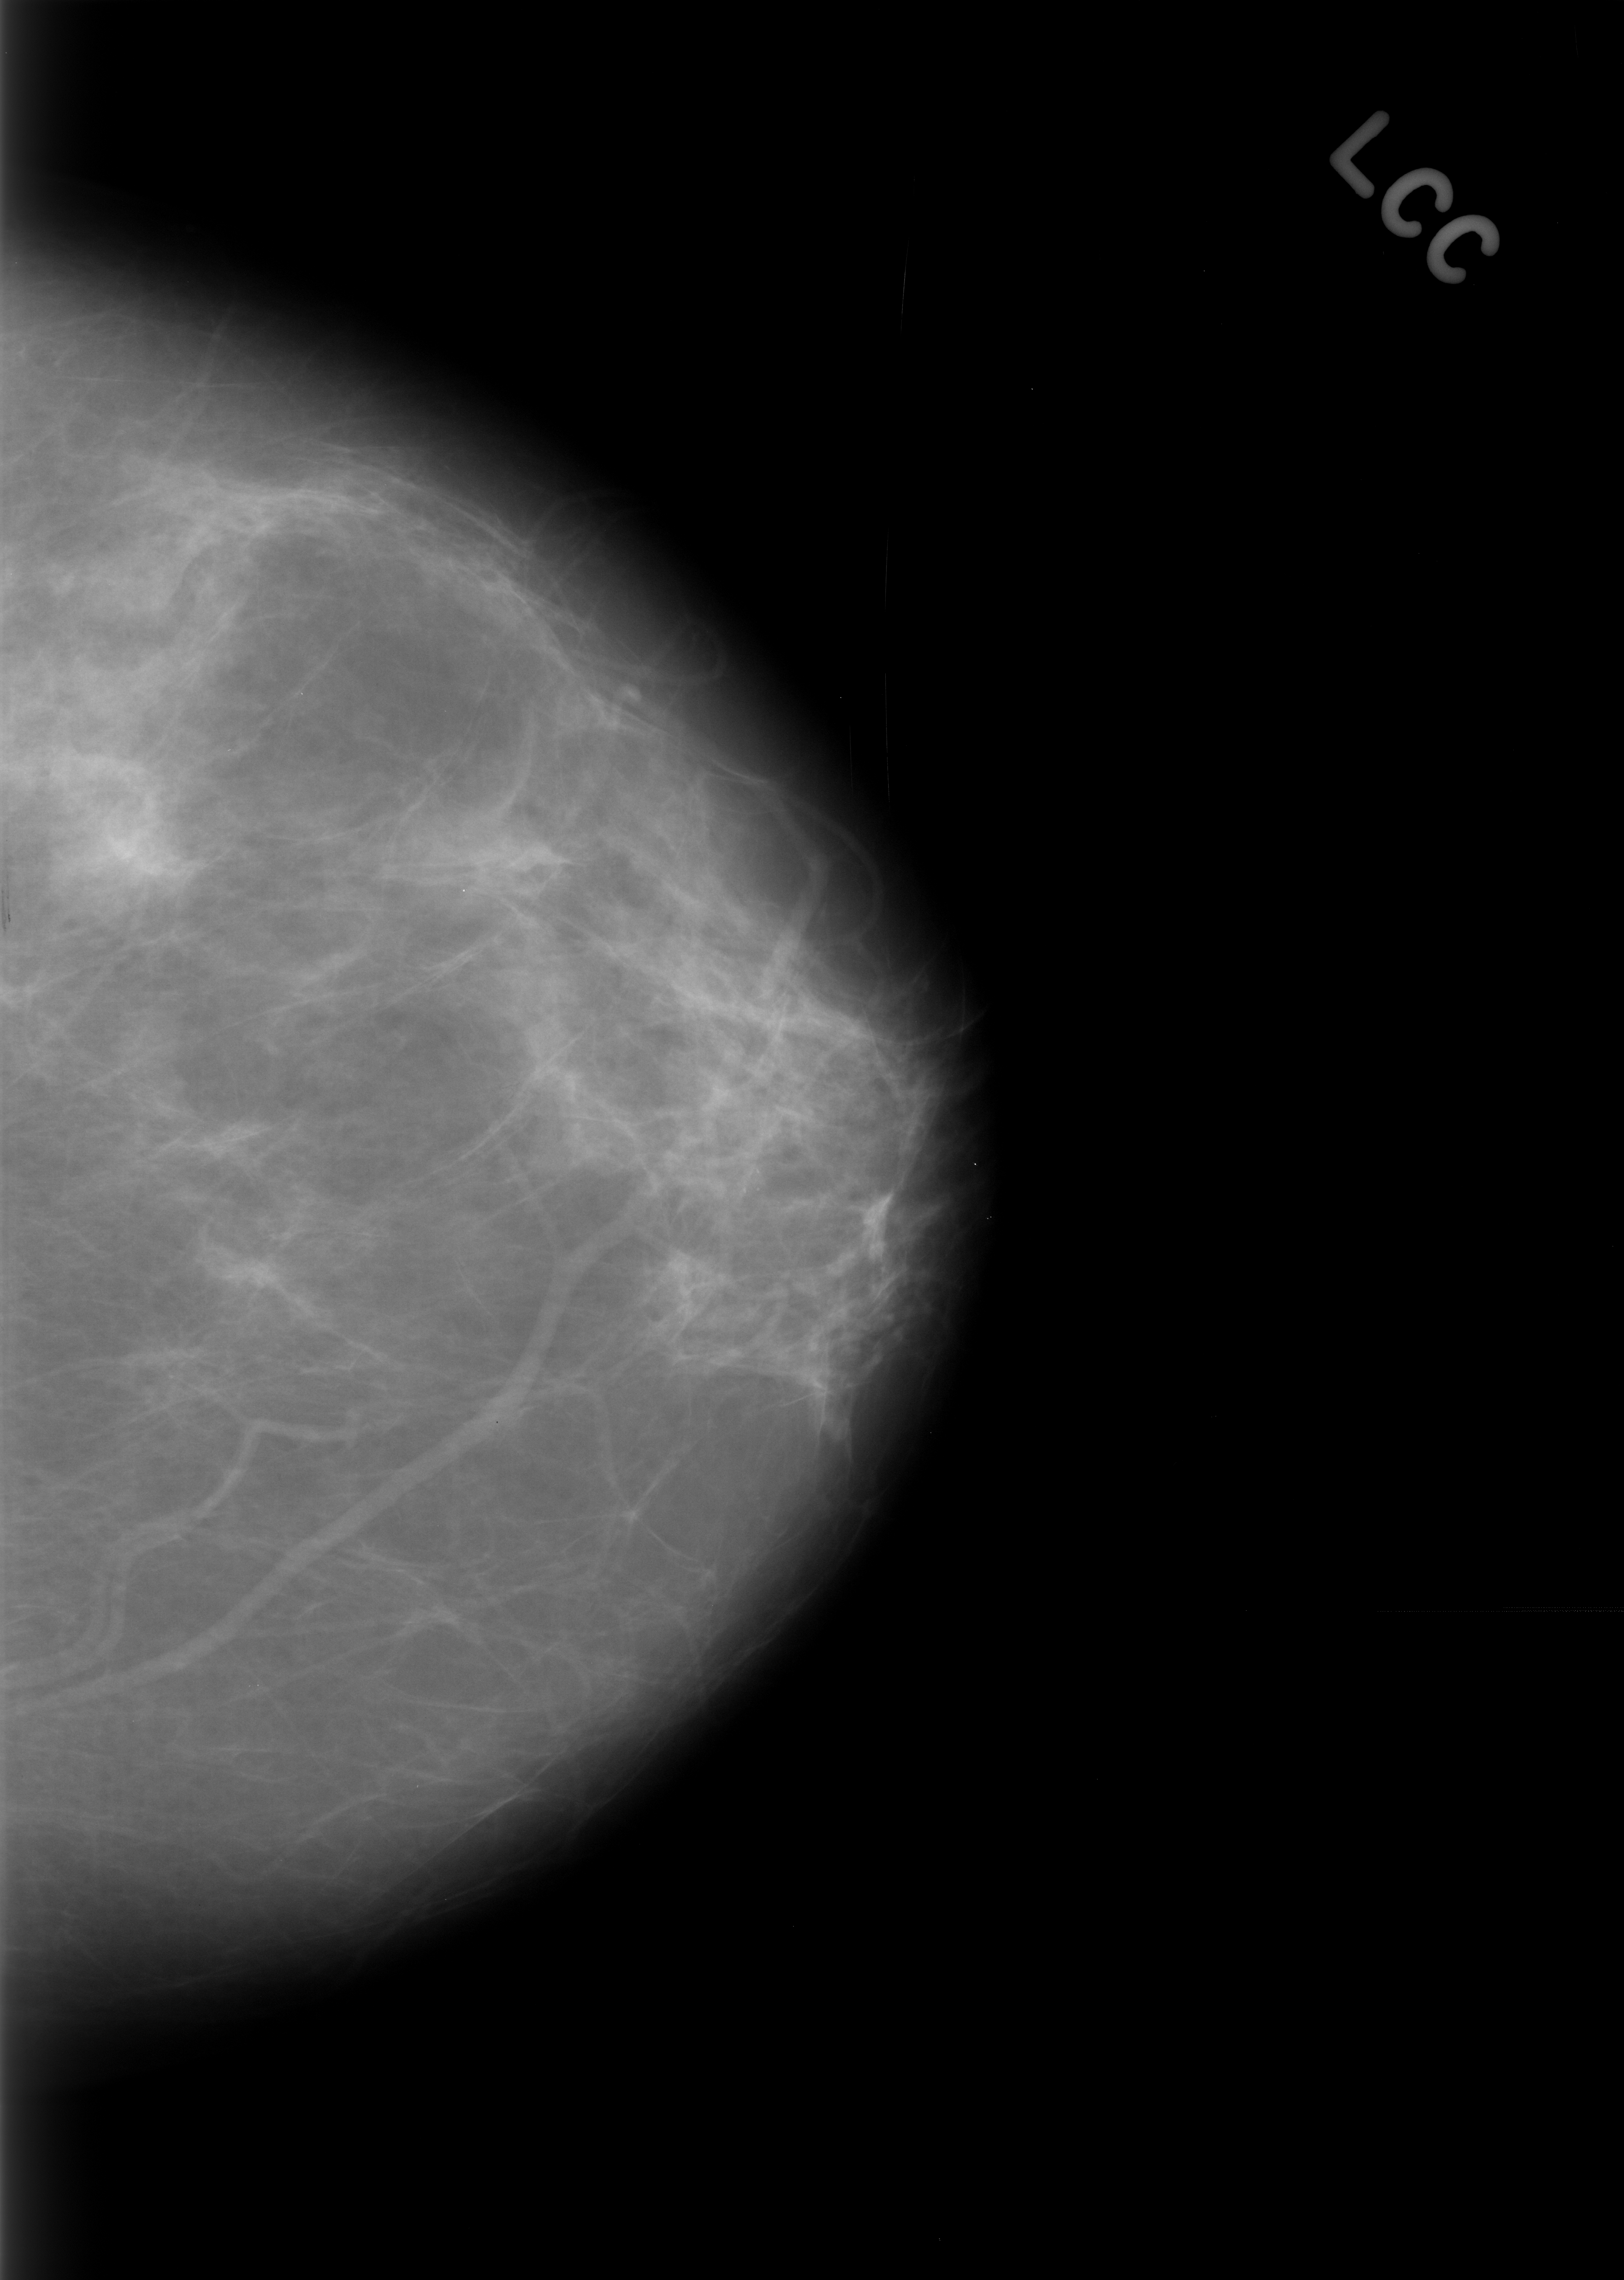
Scanned film-screen mammogram; left breast; CC view; BI-RADS breast density category 1 (scale 1–4).
Finding: mass, shape focal asymmetric density; BI-RADS assessment category 3; subtlety rating 4 on a 1 (subtle) to 5 (obvious) scale; benign without callback (not worked up further).